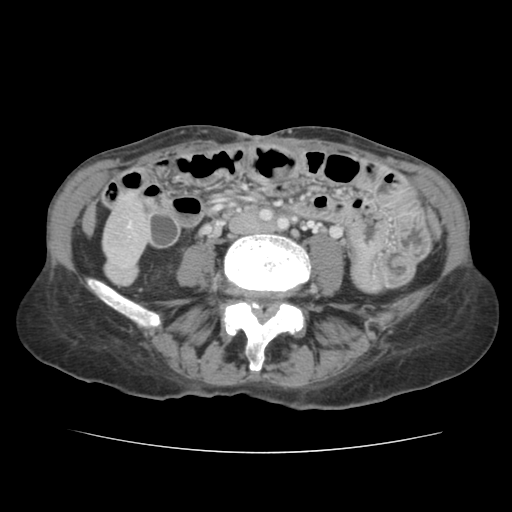
Contrast-enhanced abdominal CT, one axial slice. Slice 17 of 136 in the series (ordered by position). 120 kVp. Intravenous contrast given. Soft-tissue window (W 400 / L 40 HU). 2.5 mm slice thickness. 512 × 512 image matrix, field of view 319 × 319 mm. Female patient, age 77 years. From the clinical record (not read from this slice): diagnosis: colorectal cancer liver metastases, imaged before liver resection; multiple liver metastases: yes; largest metastasis: 3 cm.
Structures marked on this image (expert manual segmentation):
- liver: box from (x=105, y=198) to (x=147, y=275) px